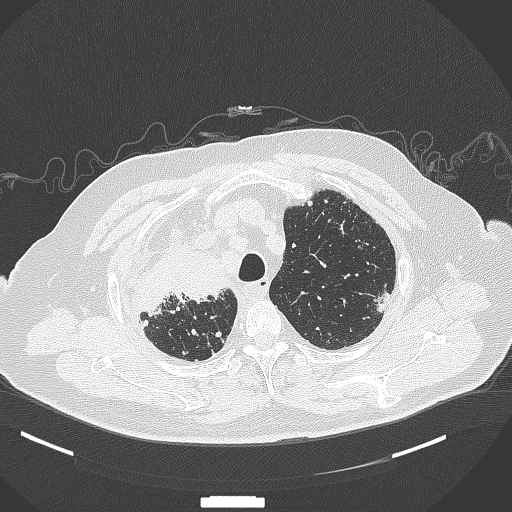
Chest CT, one axial slice. Position 298 of 384 along the scan axis. Reconstruction kernel B70f. Lung window (W 1500 / L -600 HU). 1 mm slice thickness. 512 × 512 image matrix, field of view 400 × 400 mm. Patient: male, 69 years. From the clinical record (not read from this slice): clinical TNM (as recorded): T4 N3 M1.
Structures marked on this image (rectangle marked by the reading radiologist):
- lung tumour (recorded histology: adenocarcinoma): bounding box <130,245,236,314> (left, top, right, bottom; pixels)